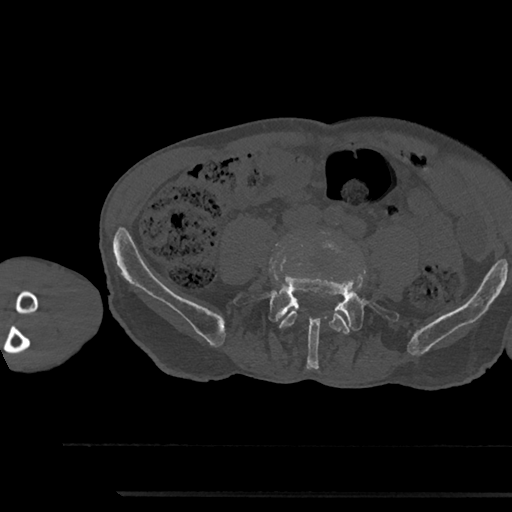
CT including the spine, one axial slice. Slice 371 of 797 in the series (ordered by position). Reconstruction kernel Br40s/3. 120 kVp. Bone window (W 1800 / L 400 HU). 512 × 512 image matrix. Patient: male, 79 years. Case-level facts recorded for this patient, not image findings: primary cancer: prostate.
Outlined on this slice (semi-automatically segmented with operator editing):
- L4 vertebra: bounding box <279,239,350,334> (left, top, right, bottom; pixels)
- L5 vertebra: <234,265,400,369>